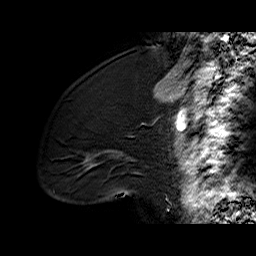
Breast MRI (dynamic contrast-enhanced), one sagittal slice; position 20 of 60 along the scan axis; dynamic contrast-enhanced series, time point 2 of 6 at this slice position (early post-contrast); 1.5 T; TE 6.2 ms, TR 32.4 ms; 256 × 256 image matrix, field of view 200 × 200 mm. Female patient. From the clinical record (not read from this slice): setting: breast cancer imaged before/during neoadjuvant chemotherapy; receptor status: triple-negative.
Annotated regions visible in this slice (semi-automatic segmentation, software-assisted and operator-edited):
- analysis volume of interest (the breast-tissue region the enhancement analysis was run in; not a lesion): bounding box <48,102,134,196> (left, top, right, bottom; pixels)
- tumour enhancement mask (voxels above the 100 % enhancement threshold inside the analysis volume of interest): <104,150,123,155>